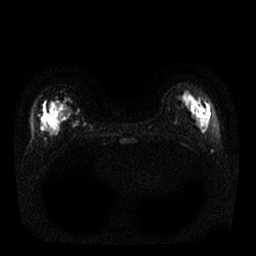
Breast MRI, one axial slice. Diffusion-weighted series; image 2 of 4 stored at this slice position (different b-values; order by instance number). 1.5 T. 256 × 256 image matrix, field of view 340 × 340 mm. Female patient.
Structures marked on this image (outlined manually by an expert reader):
- tumour on diffusion-weighted imaging: box from (x=43, y=110) to (x=53, y=134) px